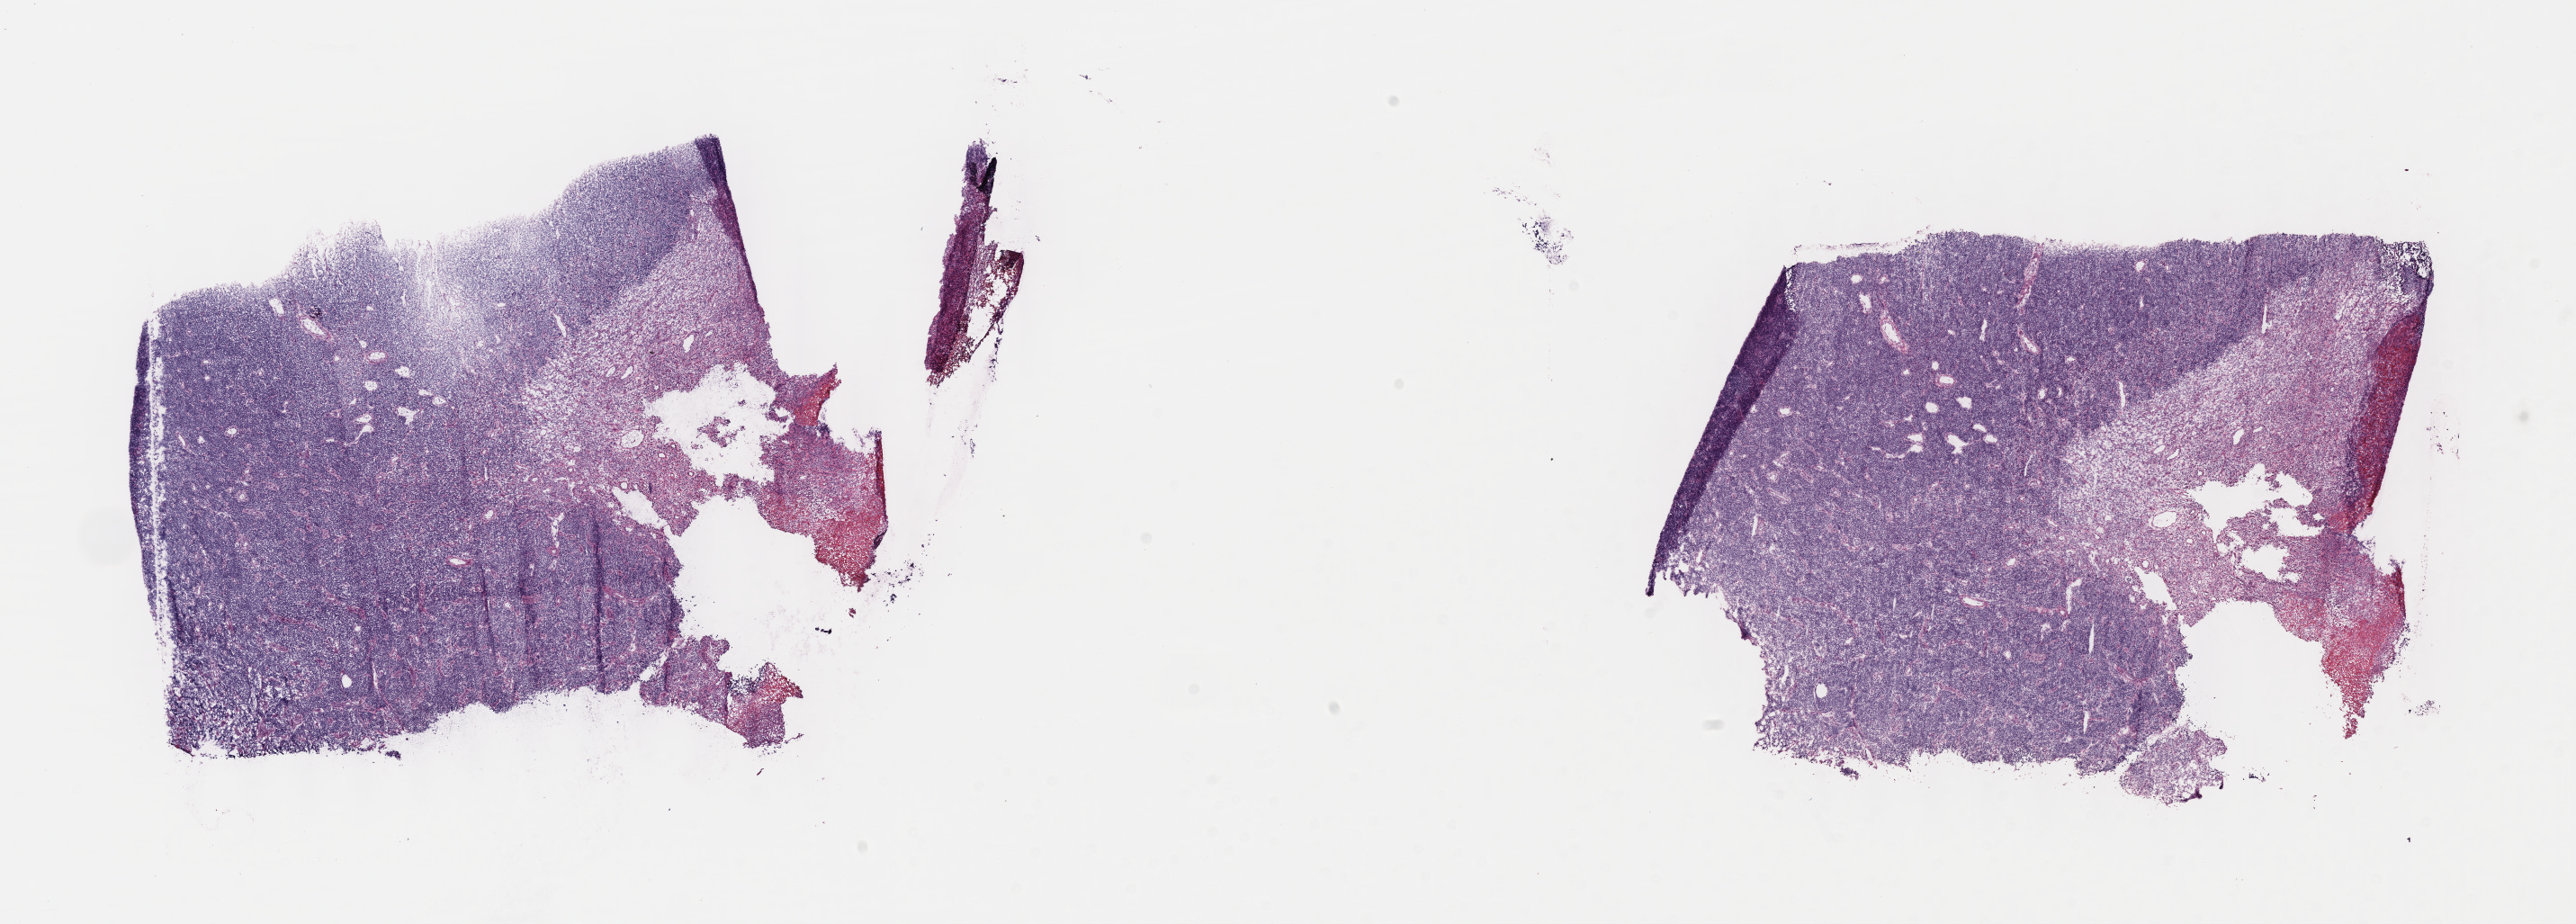
Hematoxylin and eosin (H&E) whole-slide image — whole scanned area (about 23.1 x 8.3 mm) shown as a low-resolution overview. Frozen section. Specimen: primary tumor. Site: cranium. Patient: female, age at initial diagnosis 6 years. Slide review estimates, as recorded: tumor cells 90%, tumor nuclei 90%, stromal cells 10%, necrosis 0%, normal cells 0%. Infiltration values recorded for this section: lymphocyte infiltration 10%, monocyte infiltration 15%, neutrophil infiltration 0%.
Ann Arbor stage (patient): Stage III. Section: top of the tissue portion. Diagnosis: Burkitt lymphoma, NOS.